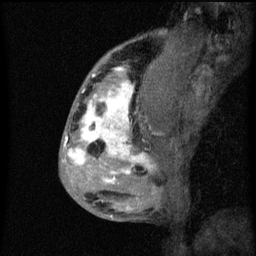
Breast MRI (dynamic contrast-enhanced), one sagittal slice. Slice 23 of 60 in the series (ordered by position). Dynamic contrast-enhanced series, image 2 of 3 at this slice position (ordered by acquisition). 1.5 T. TE 4.2 ms, TR 8 ms. 2 mm slice thickness. 256 × 256 image matrix, field of view 180 × 180 mm. Patient: female, 50 years.
Outlined on this slice (semi-automatic segmentation, software-assisted and operator-edited):
- analysis volume of interest (the breast-tissue region the enhancement analysis was run in; not a lesion): box from (x=66, y=64) to (x=141, y=187) px
- tumour enhancement mask (voxels above the 70 % enhancement threshold inside the analysis volume of interest): (x=66, y=68)–(x=141, y=183)